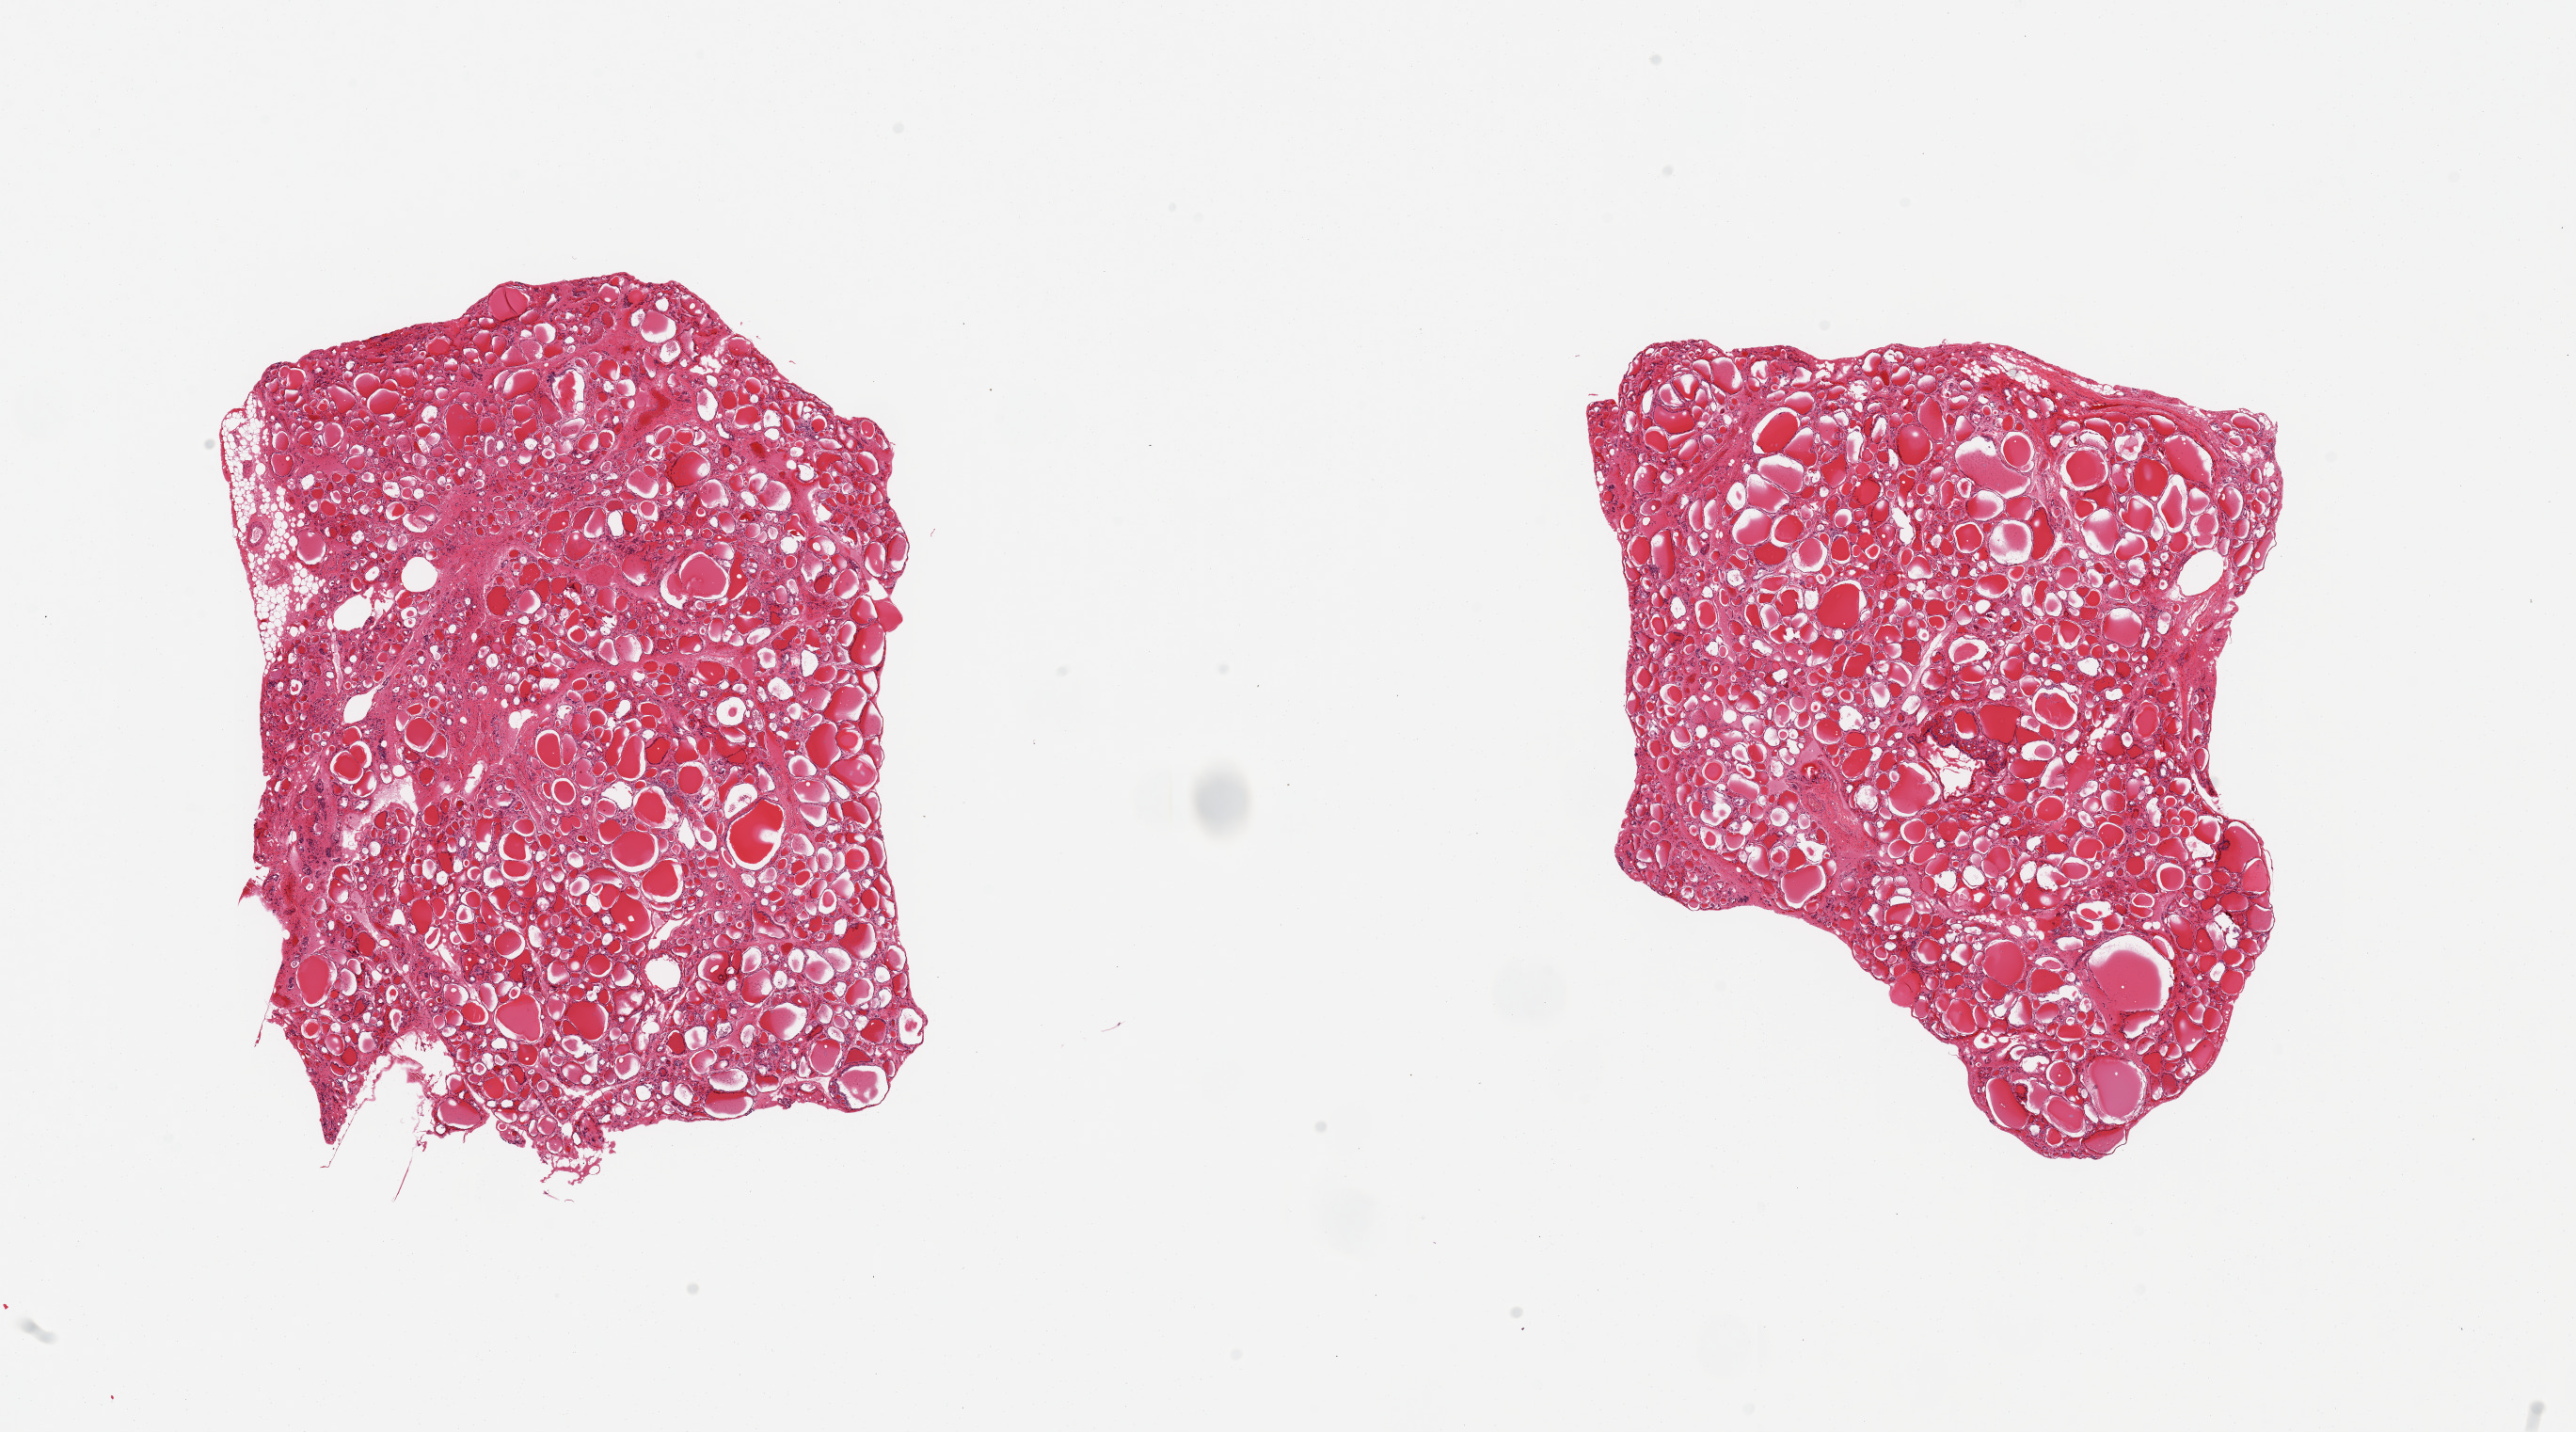
Whole-slide image, H&E stain — low-resolution overview of the scanned area, about 21.7 x 12.0 mm. PAXgene-fixed paraffin-embedded (PFPE) section. Sampled site (target tissue): thyroid. Donor tissue sample. Donor: male.
Review note (as recorded): 2 pieces.